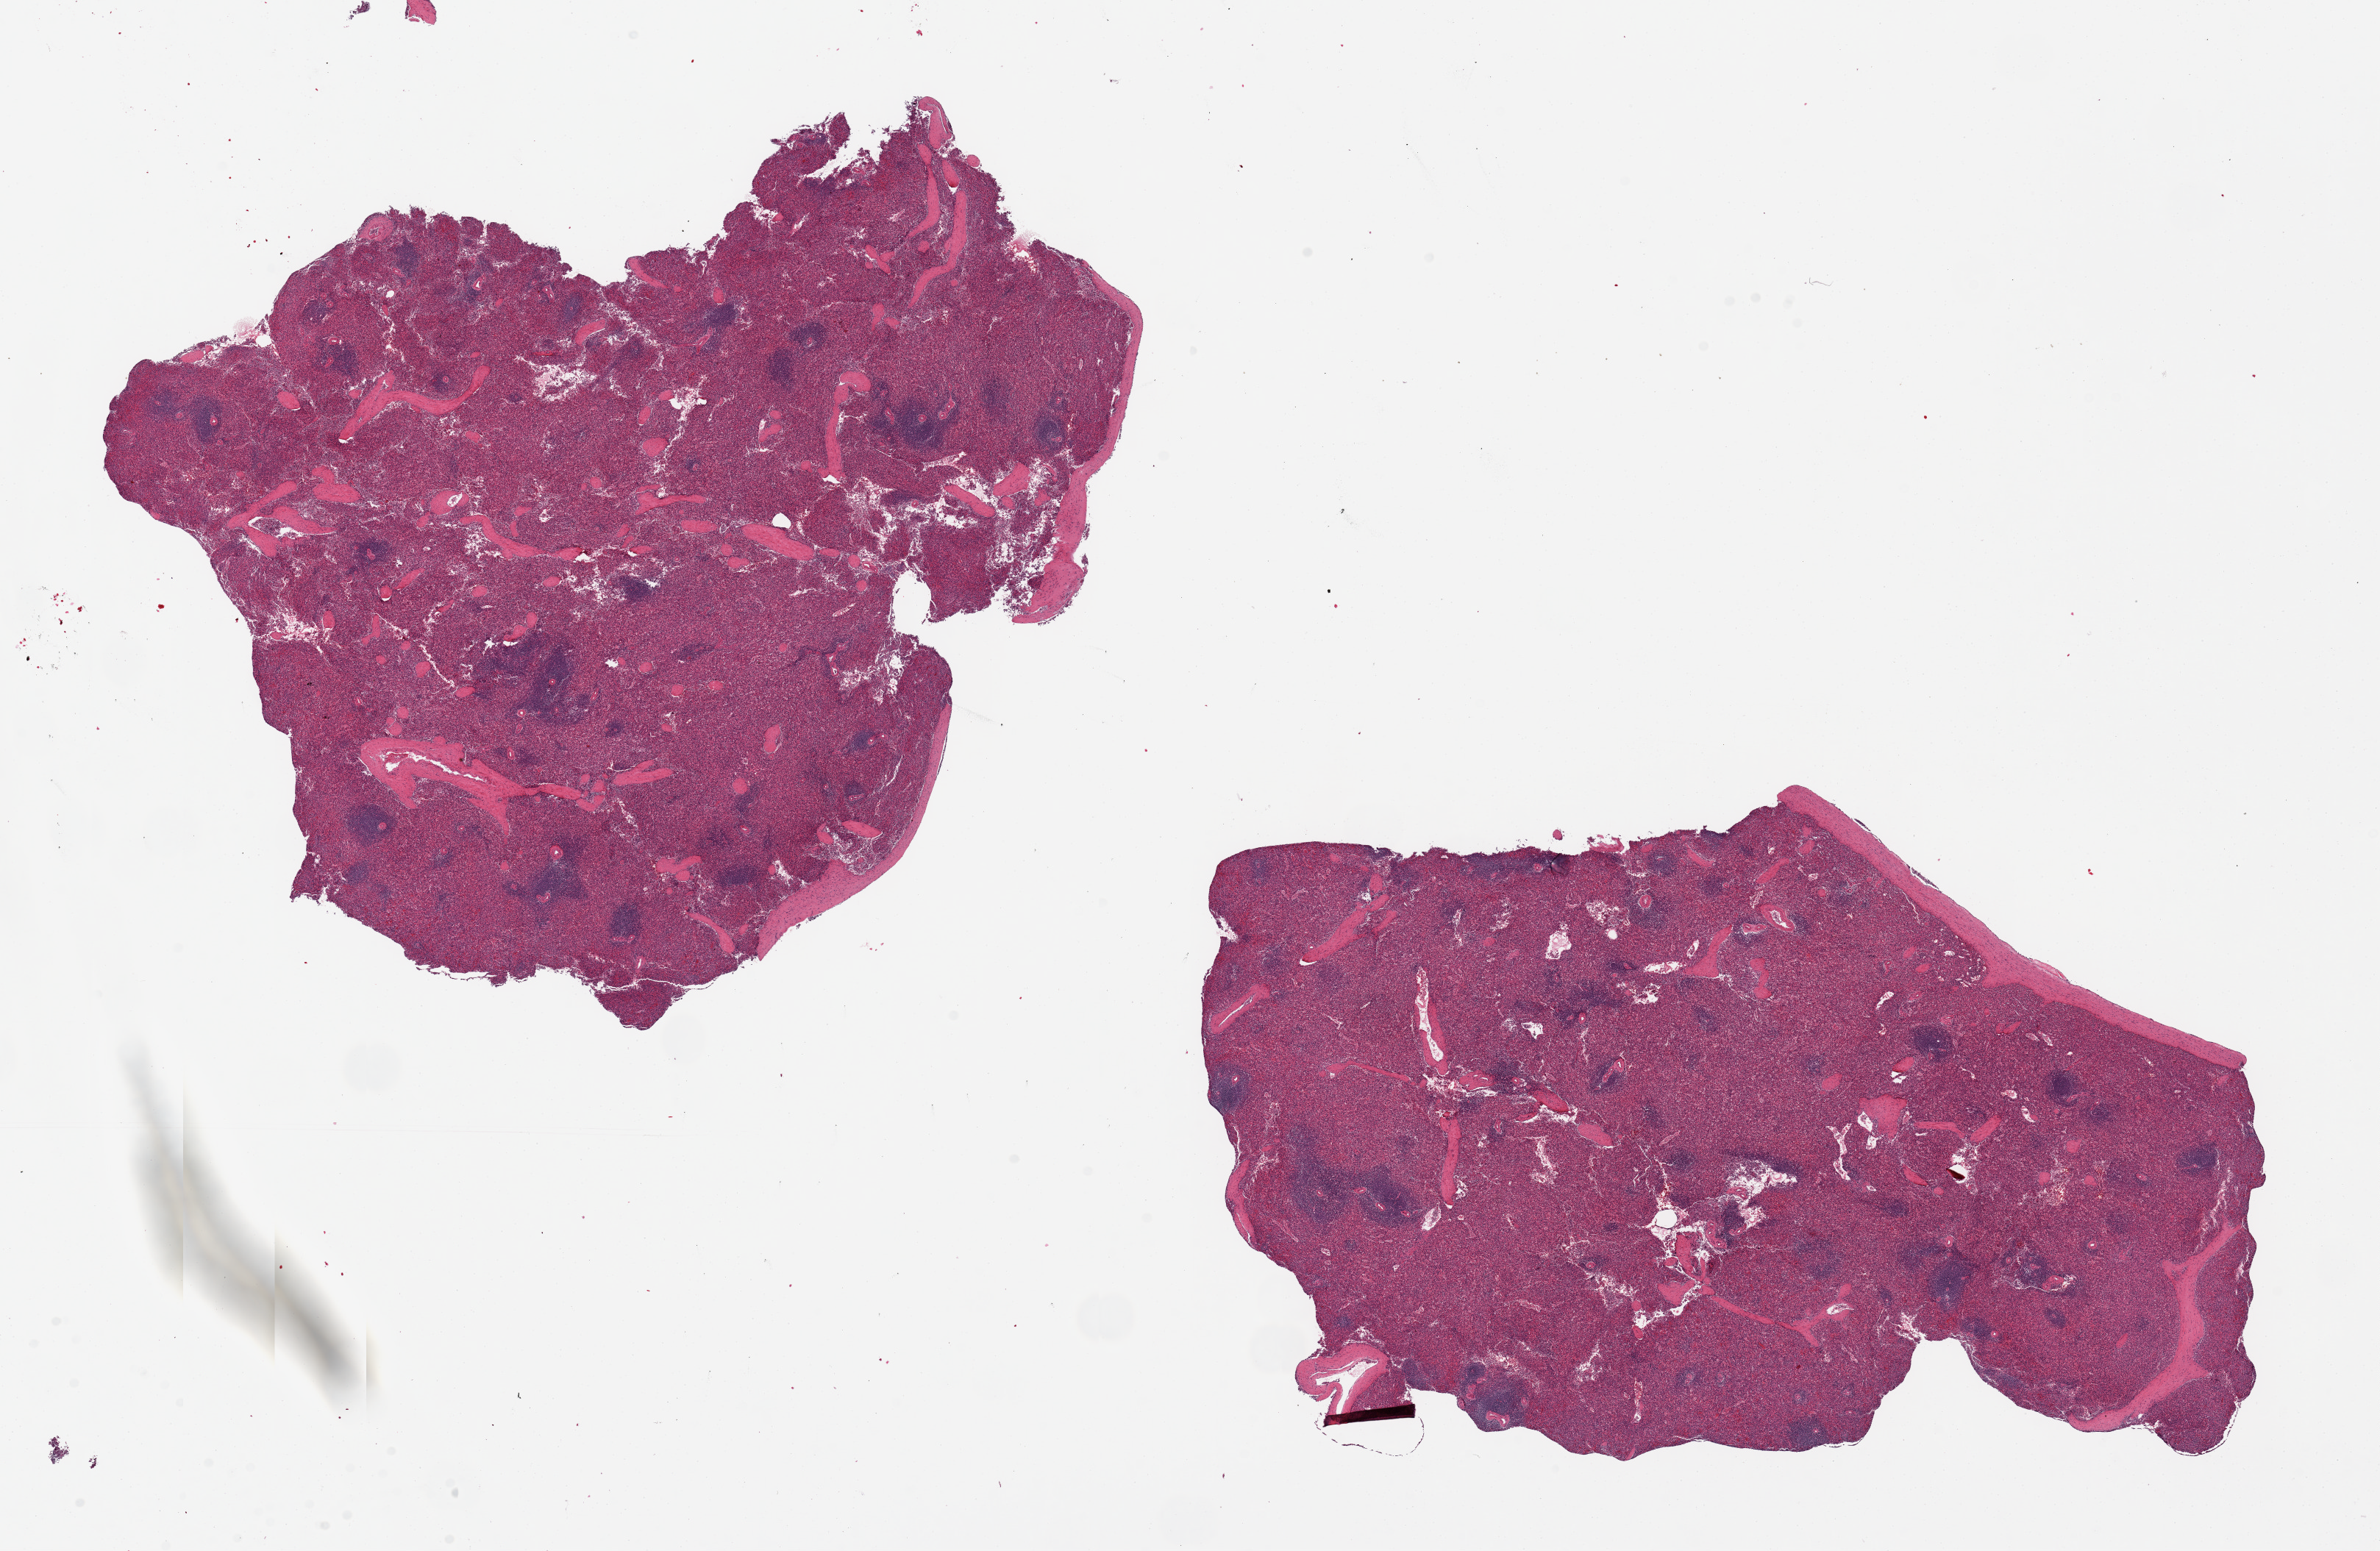
Whole-slide image, haematoxylin and eosin stain, shown as a low-resolution overview of the whole scanned area (about 25.6 x 16.7 mm, slide scanned at 20x). PAXgene-fixed, paraffin-embedded tissue. Target tissue: spleen. Tissue donor sample. Donor sex: female.
Review note (as recorded): 2 pieces. 11x10 & 12x8mm; Focally fragmented.